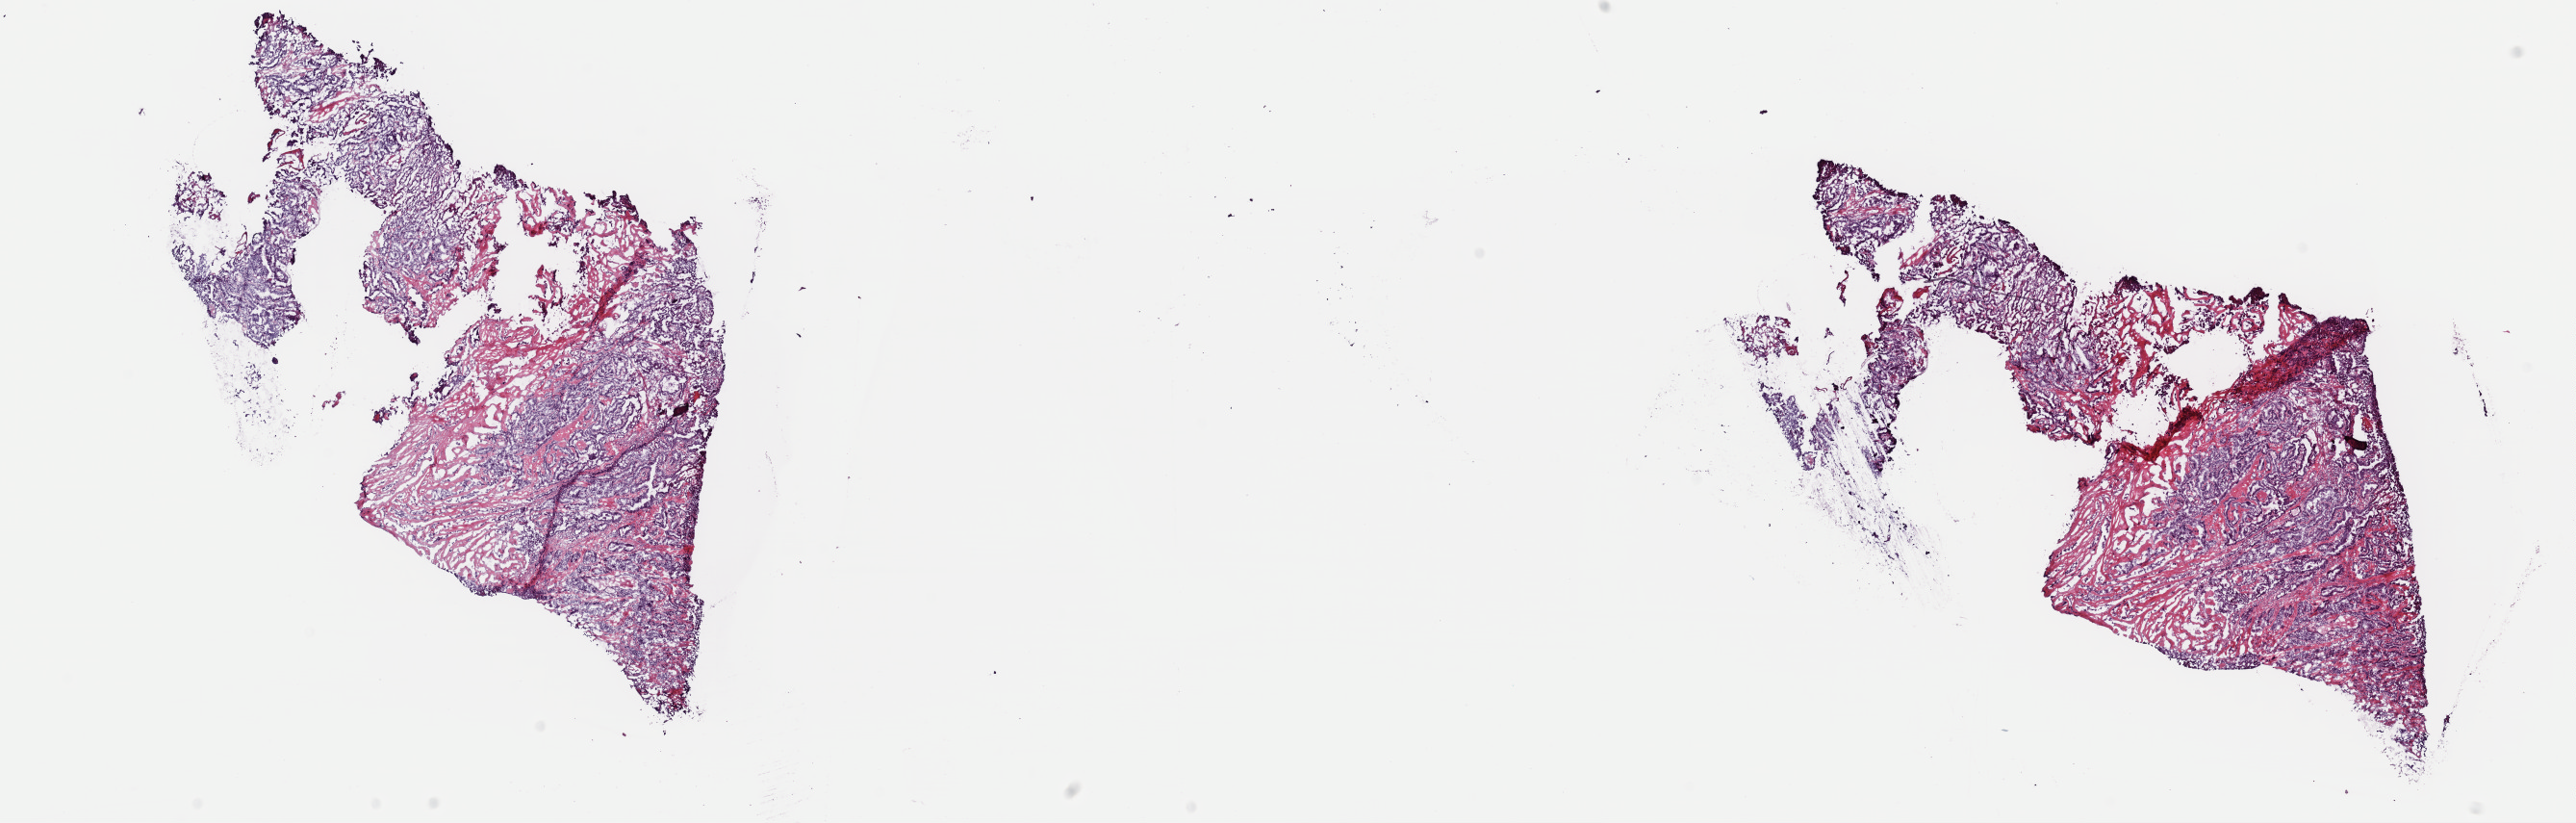
Whole-slide histology image, H&E-stained — shown as a low-resolution overview of the whole scanned area (about 21.1 x 6.8 mm). Frozen section. Thyroid, primary tumour sample. Male patient; age at initial diagnosis 57 years.
Histologic diagnosis: Papillary adenocarcinoma, NOS (thyroid gland).